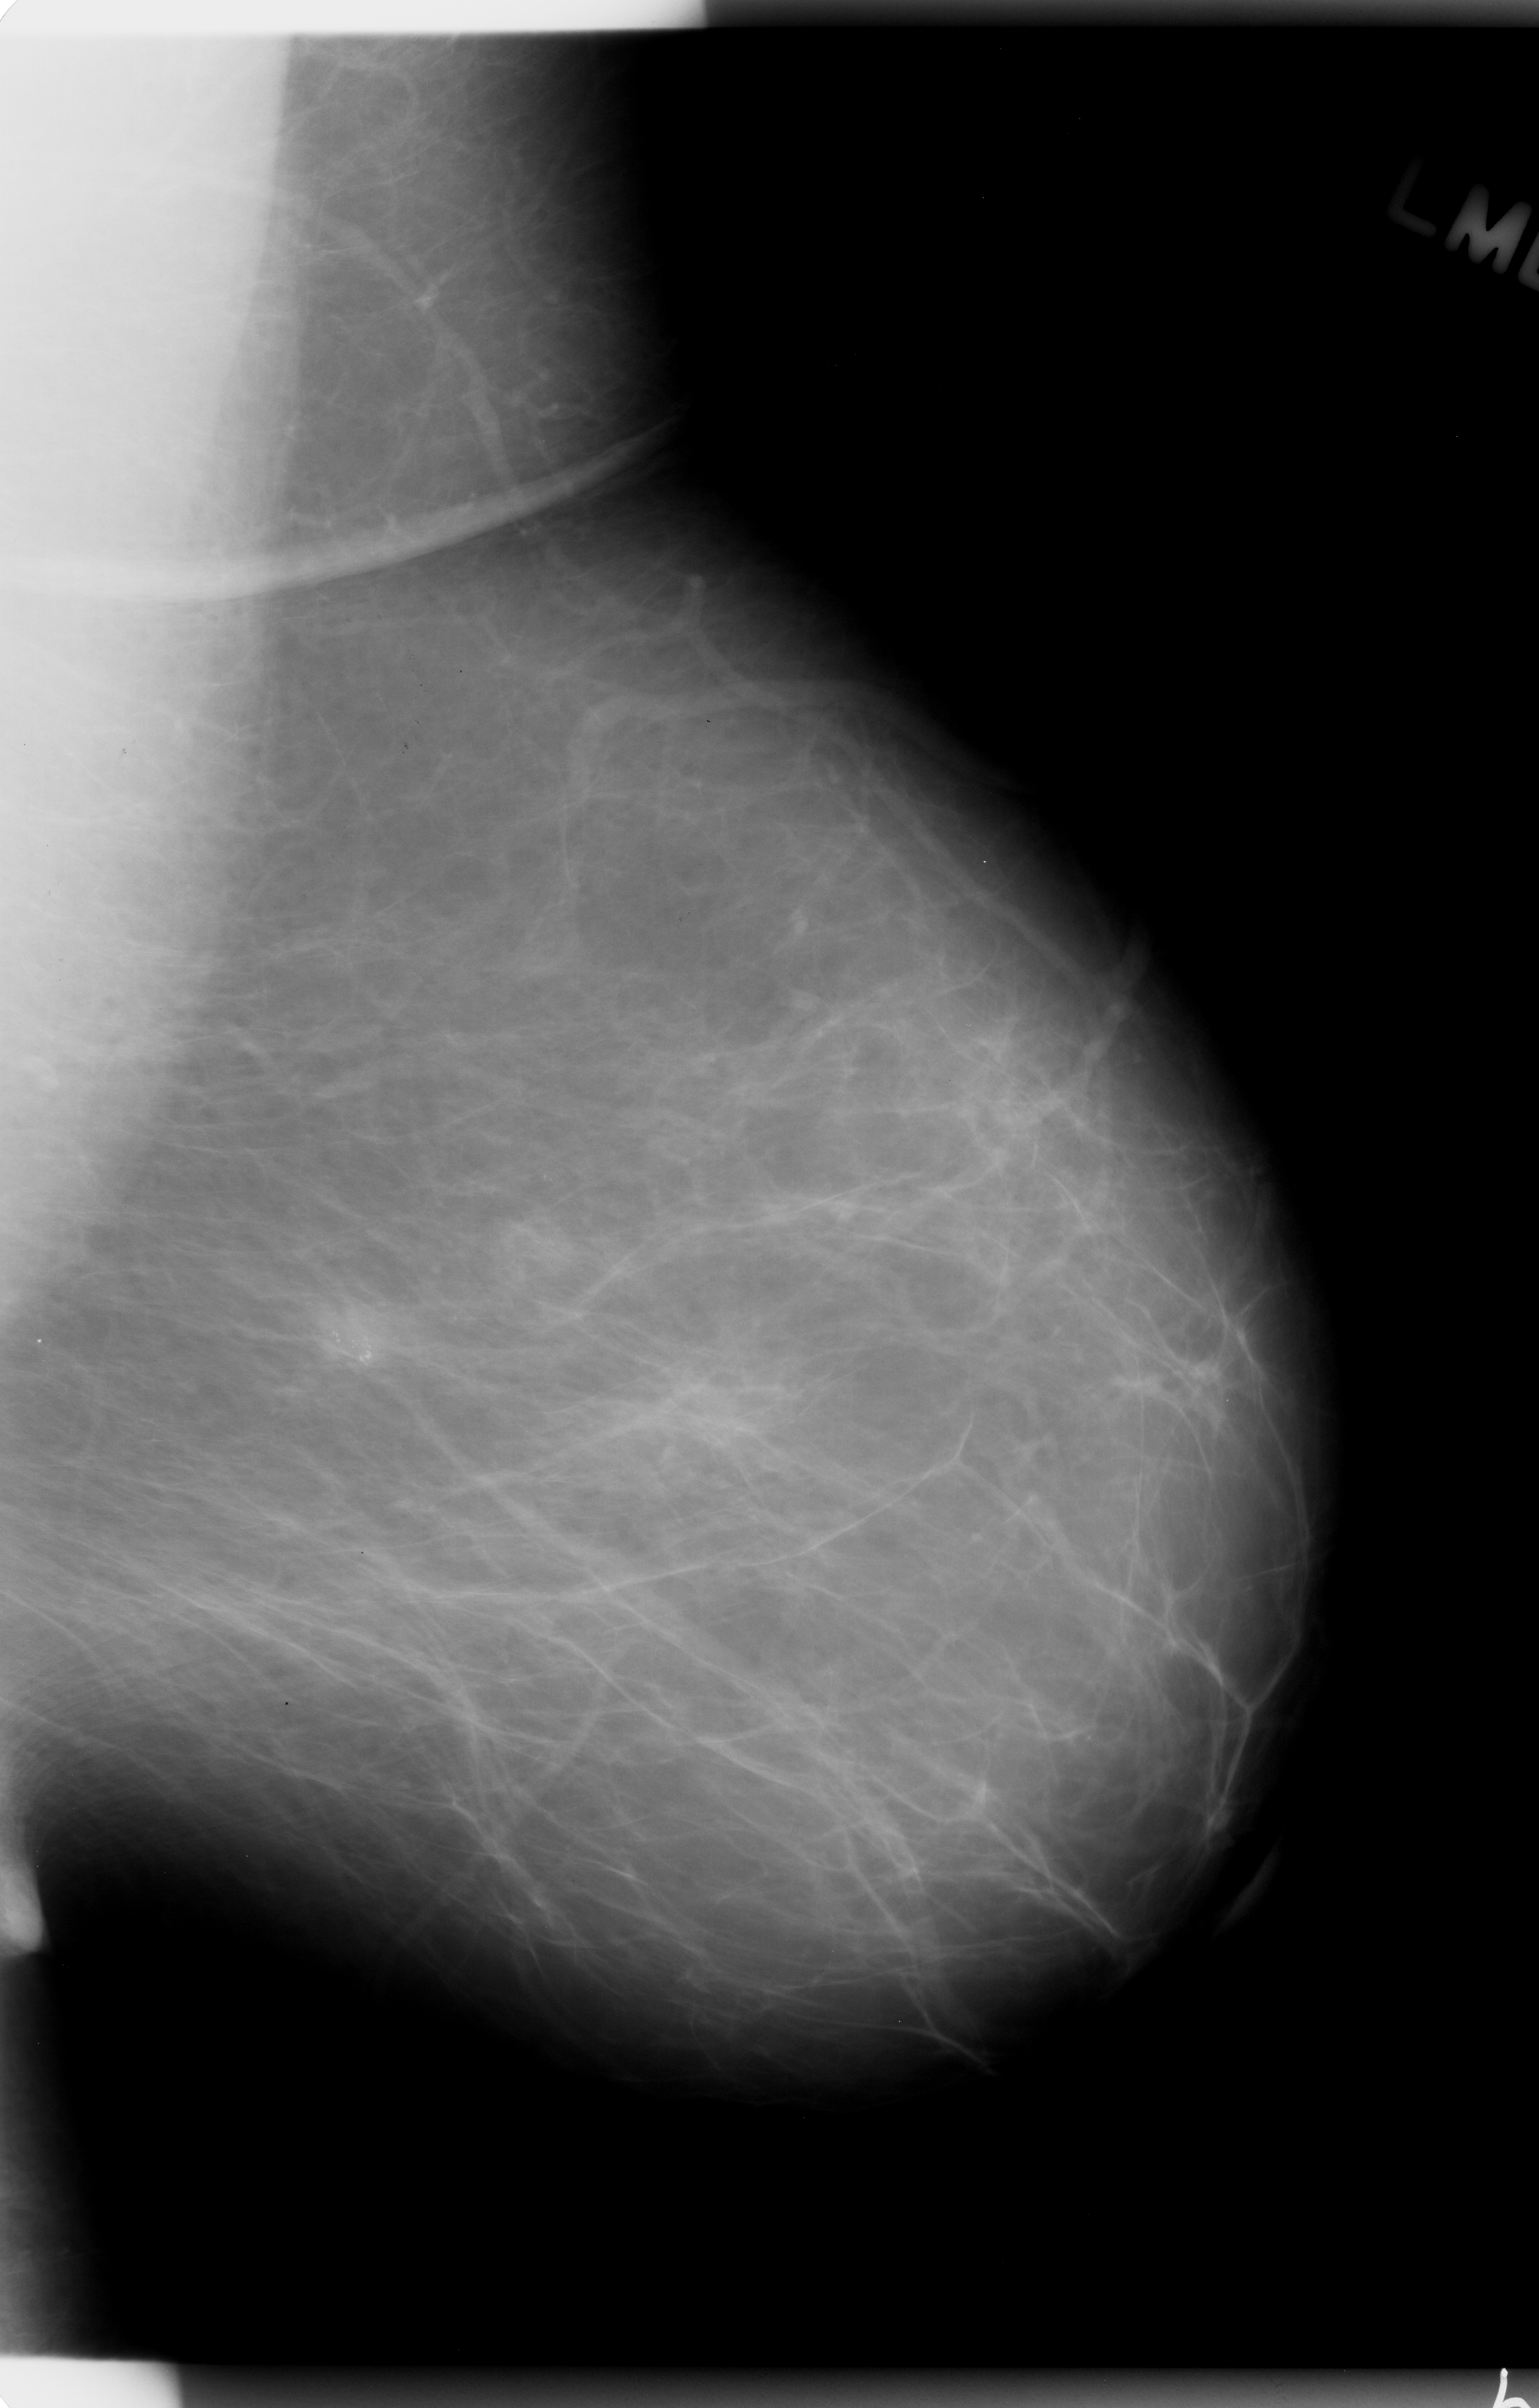
Scanned film-screen mammogram; left breast; mediolateral oblique (MLO) view.
Marked abnormality: calcifications, morphology pleomorphic, distribution clustered; BI-RADS assessment category 4; pathology (as recorded): malignant.